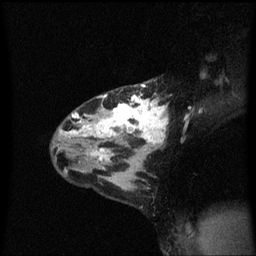
Breast MRI (dynamic contrast-enhanced), one sagittal slice. Slice 39 of 60 in the series (ordered by position). Dynamic contrast-enhanced series, image 2 of 3 at this slice position (ordered by acquisition). 1.5 T. TE 4.2 ms, TR 8.4 ms. 2 mm slice thickness. 256 × 256 image matrix, field of view 200 × 200 mm. Patient: female, 32 years.
Outlined on this slice (semi-automatic segmentation, software-assisted and operator-edited):
- analysis volume of interest (the breast-tissue region the enhancement analysis was run in; not a lesion): bounding box (x1, y1, x2, y2) in pixels: (55, 80, 169, 167)
- tumour enhancement mask (voxels above the 70 % enhancement threshold inside the analysis volume of interest): (60, 84, 169, 161)